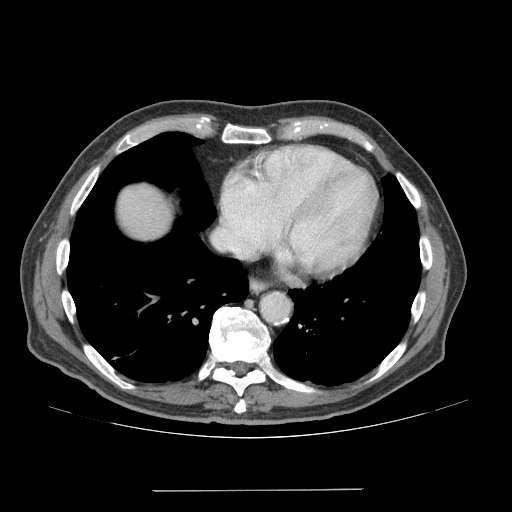
Contrast-enhanced abdominal CT (liver protocol), one axial slice. Position 69 of 77 along the scan axis. Reconstruction kernel STANDARD. Soft-tissue window (W 400 / L 40 HU). 512 × 512 image matrix. From the clinical record (not read from this slice): diagnosis: hepatocellular carcinoma (patient treated with transarterial chemoembolisation; whether this scan precedes or follows treatment is not stated here); TNM stage (as recorded): Stage-IVA; Child-Pugh class: A; tumour differentiation: well differentiated.
Outlined on this slice (semi-automatically segmented with operator editing):
- liver parenchyma outside the tumour (the mass and vessels are separate outlines, so this box may not span the whole liver): bounding box (x1, y1, x2, y2) in pixels: (118, 184, 172, 240)